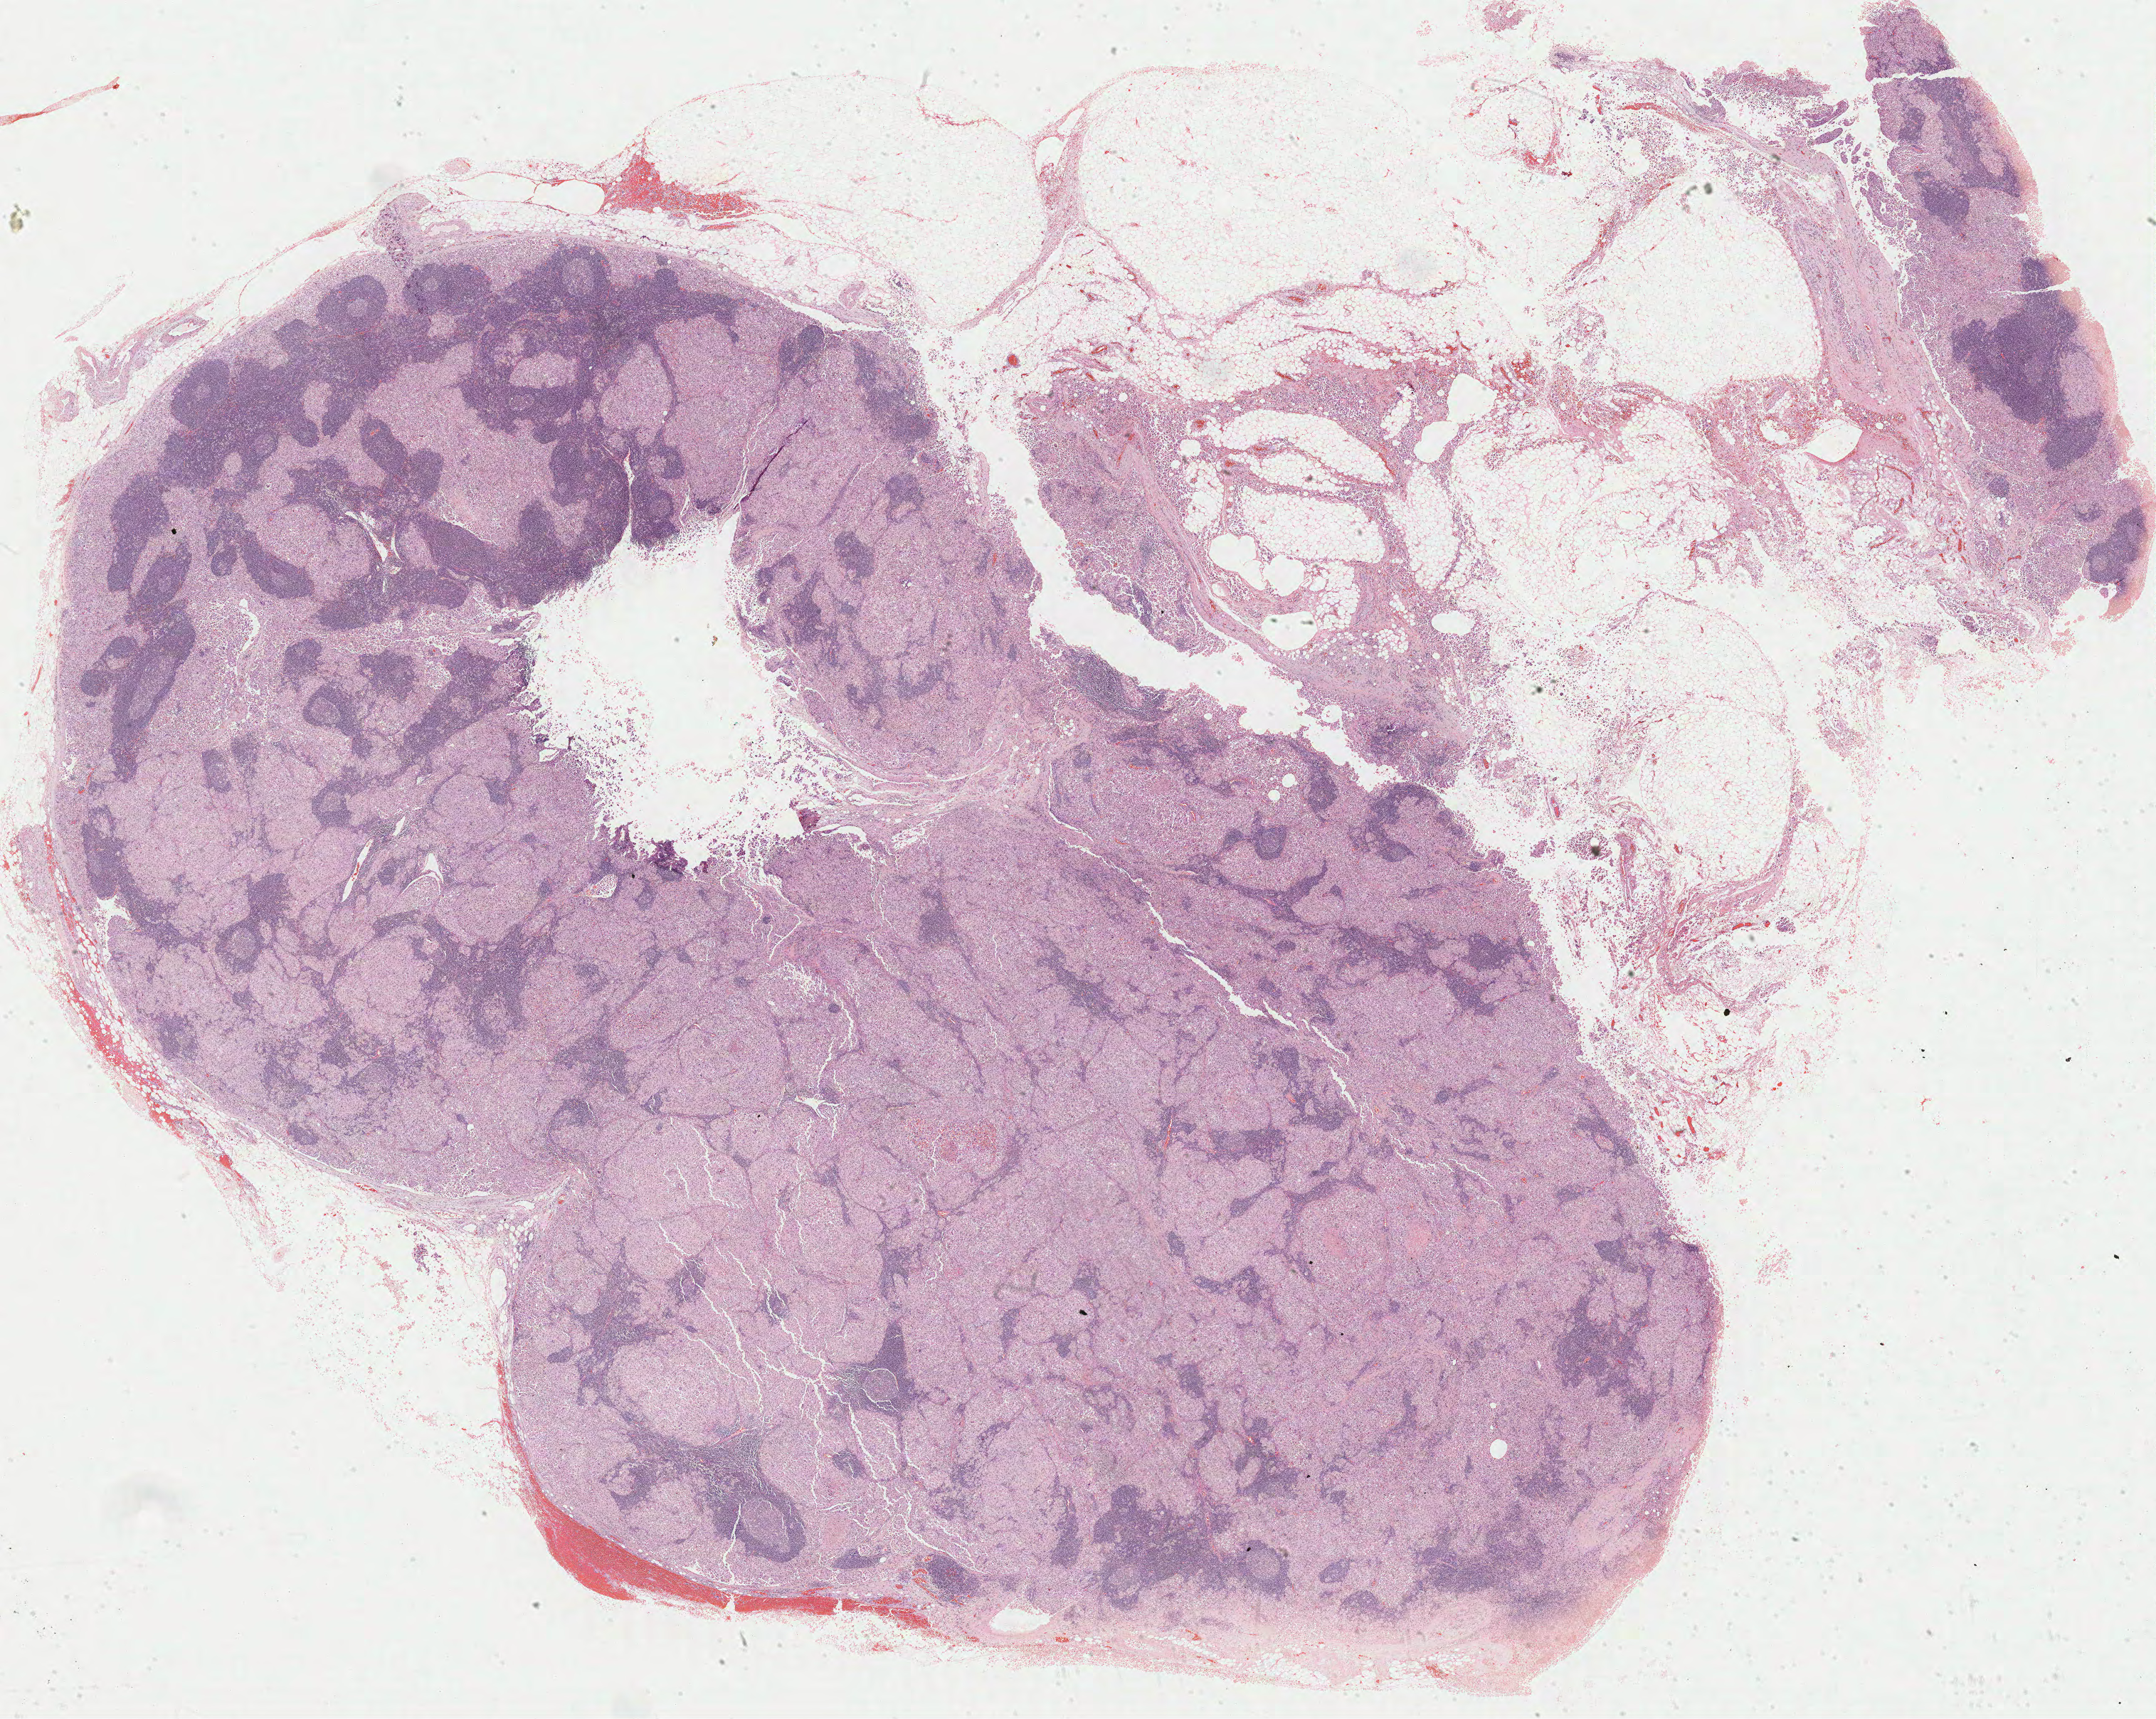
Digitized H&E tissue section (whole slide), whole scanned area (about 24.3 x 19.4 mm) shown as a low-resolution overview. Formalin-fixed paraffin-embedded (FFPE) diagnostic section. Metastatic tumour sample, sampled site not recorded. Patient sex: female.
- this section: metastatic tumour tissue
- patient diagnosis: Malignant melanoma, NOS